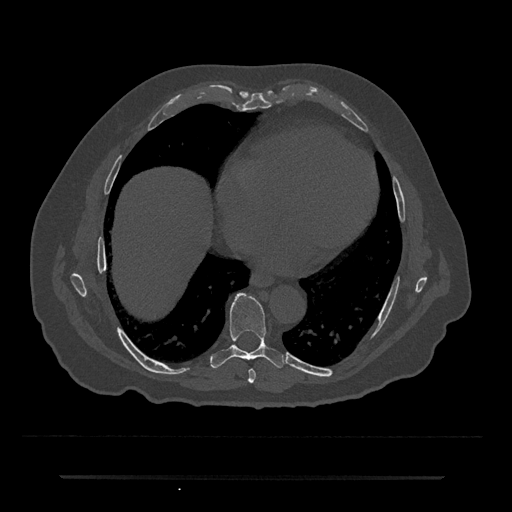
CT including the spine, one axial slice. Position 337 of 797 along the scan axis. Reconstruction kernel Br40s/3. Bone window (W 1800 / L 400 HU). 0.5 mm slice thickness. 512 × 512 image matrix. Patient: male, 69 years. Case-level facts recorded for this patient, not image findings: primary cancer: prostate.
Annotated regions visible in this slice (semi-automatic segmentation, software-assisted and operator-edited):
- T7 vertebra: bounding box <248,369,256,383> (left, top, right, bottom; pixels)
- T8 vertebra: <211,293,284,369>